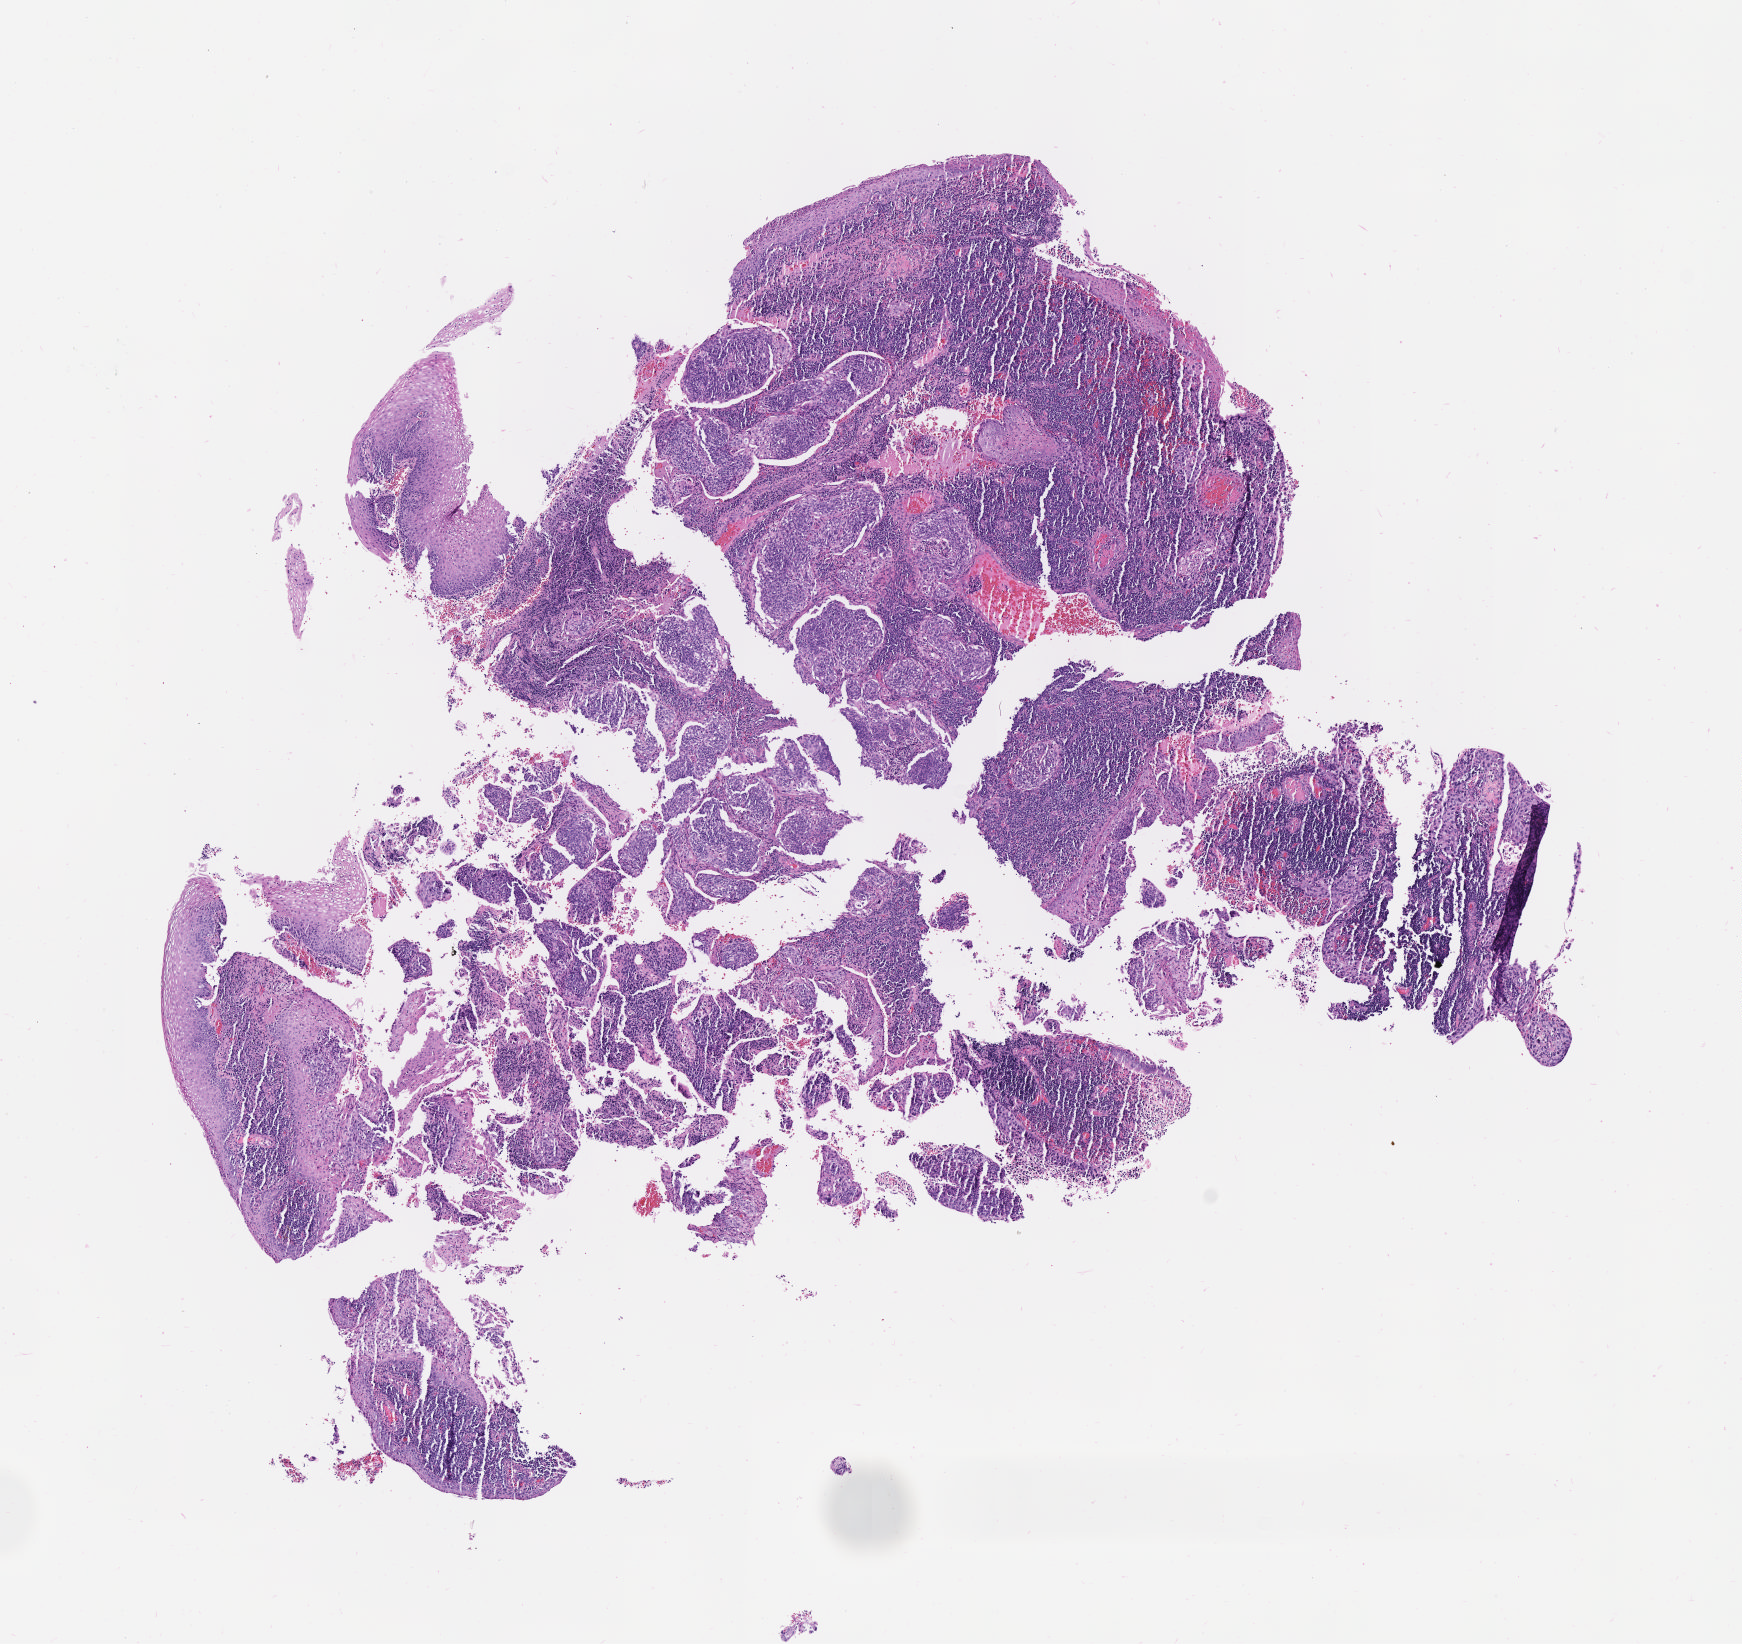
Digitized H&E-stained section, shown as a low-resolution overview of the whole scanned area (about 7.0 x 6.6 mm). Tumor tissue. Site: cervix. Female patient, 44 years old.
- histologic diagnosis: Squamous cell carcinoma, large cell, nonkeratinizing, NOS